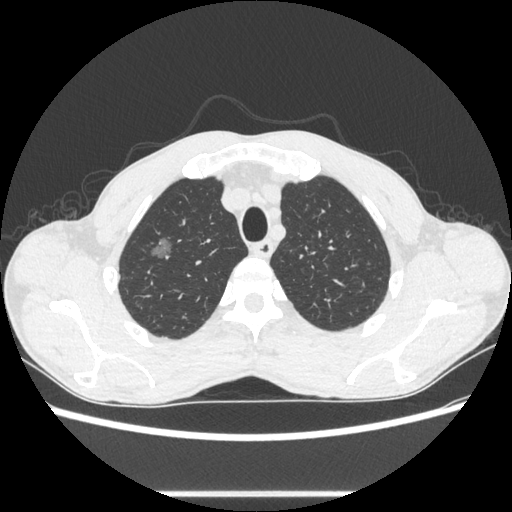
Chest CT, one axial slice. Slice 494 of 600 in the series (ordered by position). Reconstruction kernel STANDARD. 100 kVp. Lung window (W 1500 / L -600 HU). 0.62 mm slice thickness. 512 × 512 image matrix, field of view 357 × 357 mm. Patient: male, 54 years. Case-level facts recorded for this patient, not image findings: clinical TNM (as recorded): T1a N0 M0.
Structures marked on this image (rectangle marked by the reading radiologist):
- lung tumour (recorded histology: adenocarcinoma): box from (x=147, y=232) to (x=184, y=262) px